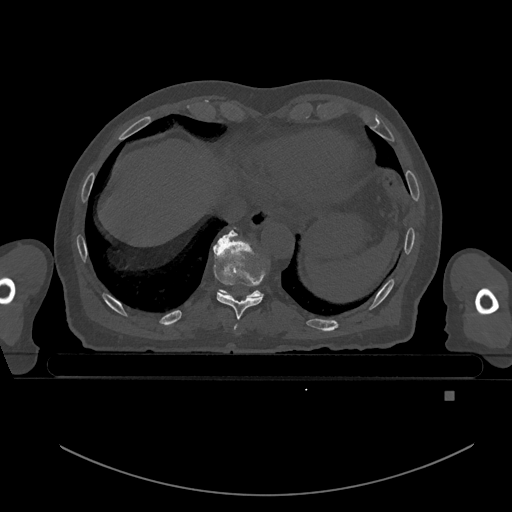
CT including the spine, one axial slice; position 132 of 969 along the scan axis; bone window (W 1800 / L 400 HU); 0.5 mm slice thickness; 512 × 512 image matrix, field of view 456 × 456 mm. Patient: male, 82 years. Case-level facts recorded for this patient, not image findings: primary cancer: prostate; vertebrae with lytic lesions (as recorded): T11, T9, T8, T2.
Outlined on this slice (semi-automatic segmentation, software-assisted and operator-edited):
- T10 vertebra: bounding box [x1, y1, x2, y2] px = [222, 228, 261, 296]
- T8 vertebra: [234, 324, 238, 332]
- T9 vertebra: [213, 230, 267, 319]